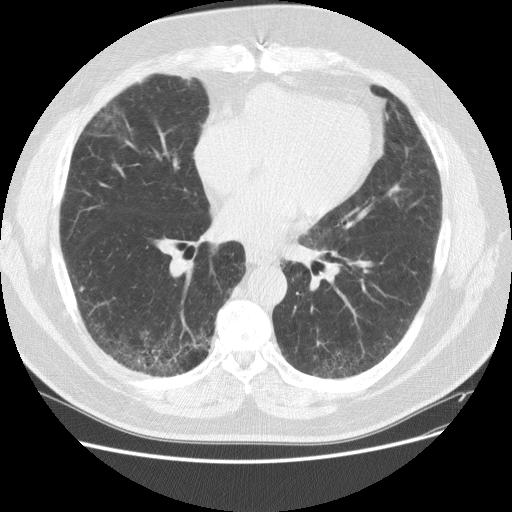
Chest CT (low-dose screening protocol), one axial image, first (baseline) screen, lung window (W 1500 / L -600 HU), 2.5 mm slice thickness, standard (soft-tissue) reconstruction kernel (STANDARD), slice 77 of 151 in the series, 512 × 512 image matrix. Male, age 59 years at enrolment.
Lesion marked by an expert reader, bounding box <84,91,131,142> (left, top, right, bottom; pixels). The screening reader recorded 2 non-calcified nodules or masses ≥4 mm on this exam (right middle lobe, right lower lobe); which of them this box marks is not recorded. Later outcome: lung cancer diagnosed 338 days after this screen — adenocarcinoma, NOS, right upper lobe, right middle lobe, moderately differentiated (G2), stage IA (AJCC 6th edition), 13 mm at pathology.